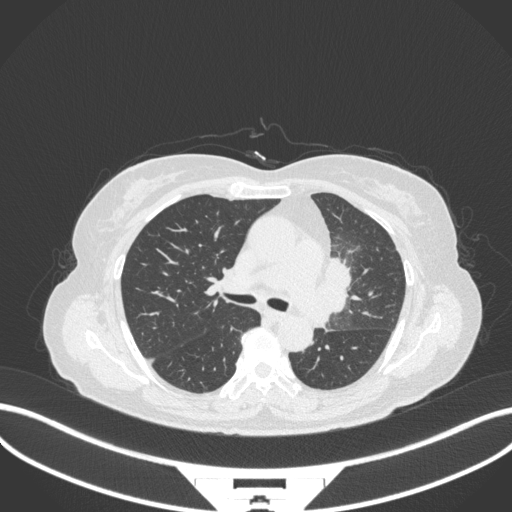
Chest CT, one axial slice. Slice 208 of 382 in the series (ordered by position). Reconstruction kernel B31f. 120 kVp. Lung window (W 1500 / L -600 HU). 1 mm slice thickness. 512 × 512 image matrix, field of view 400 × 400 mm. Patient: female, 64 years. From the clinical record (not read from this slice): clinical TNM (as recorded): T2a N2 M0.
Outlined on this slice (bounding box drawn by a radiologist):
- lung tumour (recorded histology: adenocarcinoma): bounding box [x1, y1, x2, y2] px = [315, 250, 353, 333]